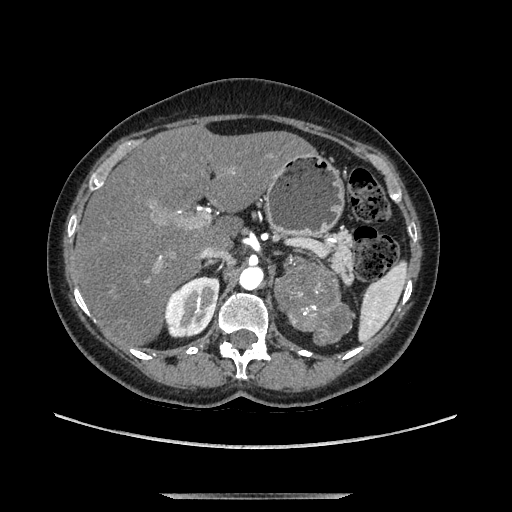
Contrast-enhanced abdominal CT, one axial slice. Slice 81 of 169 in the series (ordered by position). Soft-tissue window (W 400 / L 40 HU). 512 × 512 image matrix, field of view 400 × 400 mm. Female patient. From the clinical record (not read from this slice): diagnosis: adrenocortical carcinoma; tumour side: left adrenal; tumour size at pathology: 9 cm; Ki-67 index: 2 %; stage (as recorded): 3.
Annotated regions visible in this slice (semi-automatically segmented with operator editing):
- mass: box from (x=279, y=268) to (x=349, y=341) px